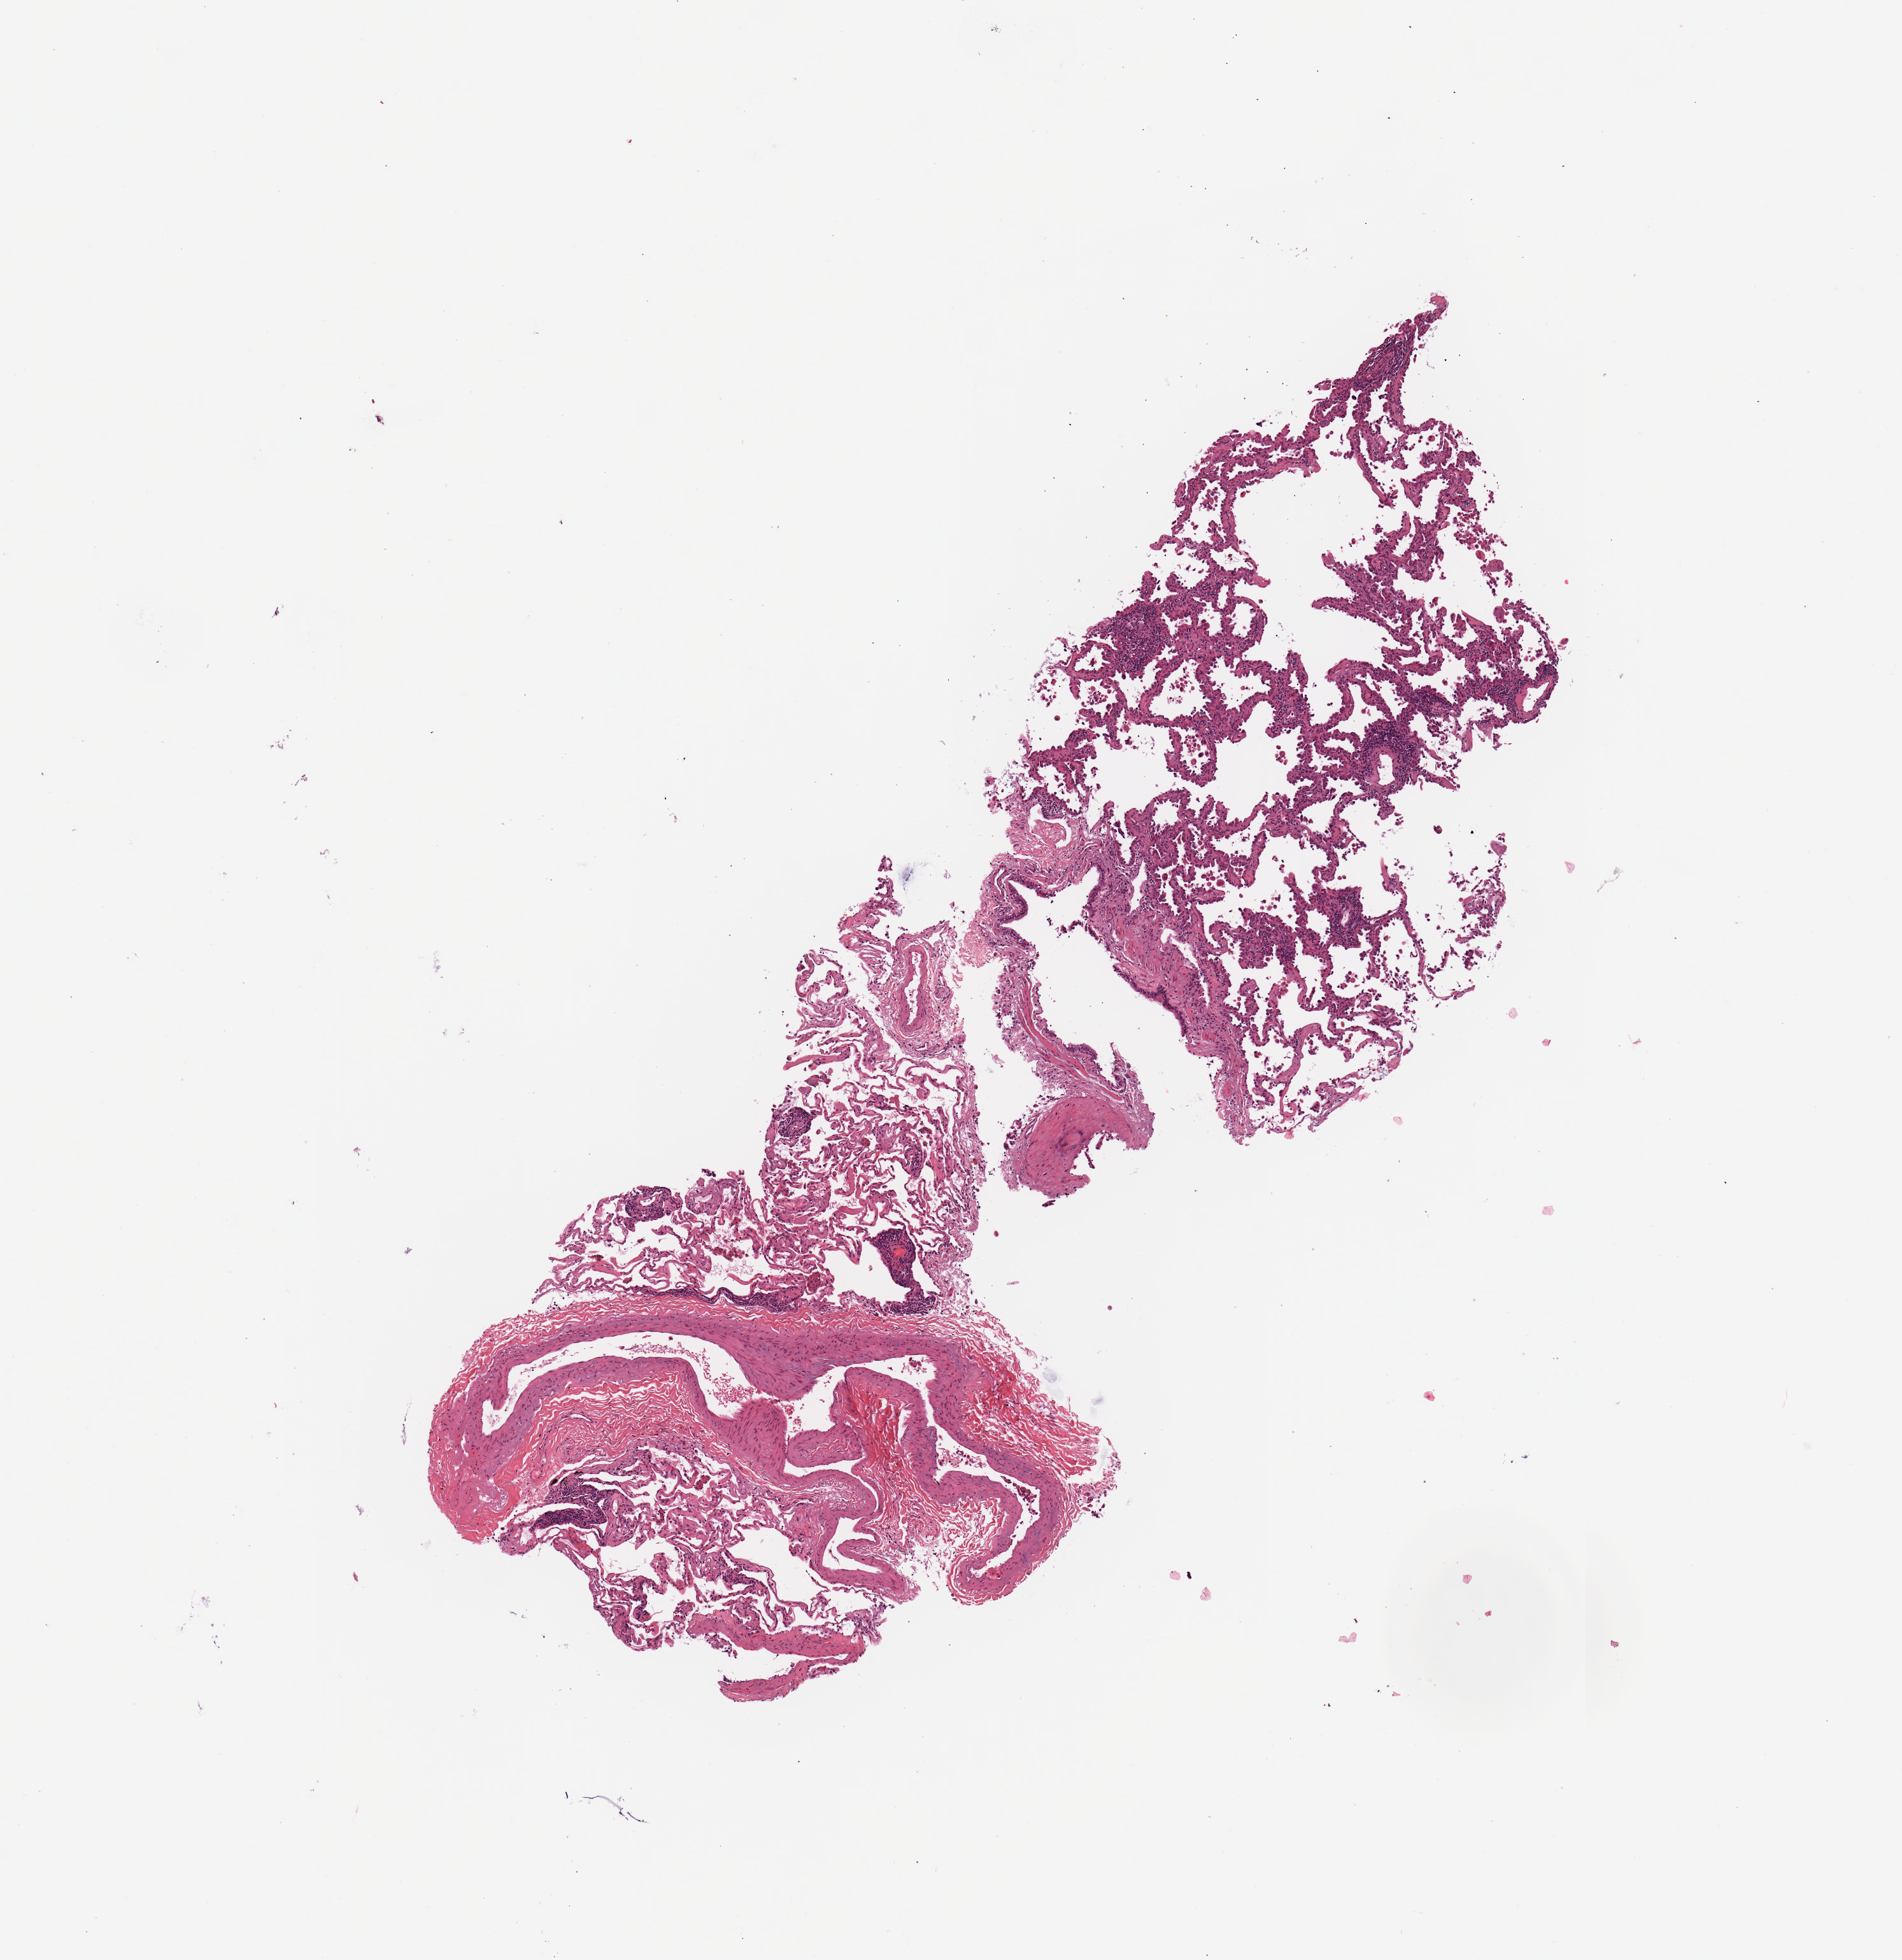
Whole-slide histology image, H&E-stained — whole scanned area (about 5.9 x 6.1 mm) shown as a low-resolution overview. Tumour tissue sample, sampled site: lung. 68-year-old female patient.
Diagnosis: Adenocarcinoma, NOS.